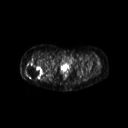
FDG PET of an extremity soft-tissue mass (from a PET/CT study), one axial slice; slice 42 of 267 in the series (ordered by position); 3.27 mm slice thickness; 128 × 128 image matrix. Patient: female, 57 years. Case-level facts recorded for this patient, not image findings: histological type: epithelioid sarcoma with vascular differentiation; site of the primary tumour: right buttock.
Outlined on this slice (expert contour drawn on MRI and transferred to this co-registered scan by the dataset authors):
- gross tumour volume (mass): bounding box [x1, y1, x2, y2] px = [24, 61, 43, 80]